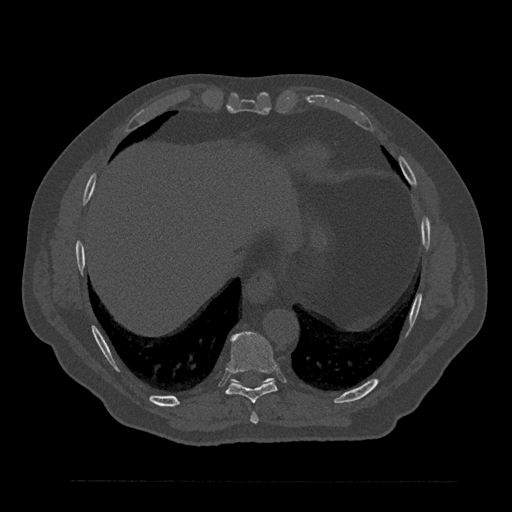
CT including the spine, one axial slice; reconstruction kernel Br40s/3; 120 kVp; bone window (W 1800 / L 400 HU); 0.5 mm slice thickness; 512 × 512 image matrix, field of view 430 × 430 mm. Male patient, age 61 years. Case-level facts recorded for this patient, not image findings: primary cancer: prostate.
Annotated regions visible in this slice (semi-automatically segmented with operator editing):
- T10 vertebra: bounding box (x1, y1, x2, y2) in pixels: (231, 378, 273, 384)
- T8 vertebra: (250, 413, 259, 424)
- T9 vertebra: (226, 332, 277, 403)